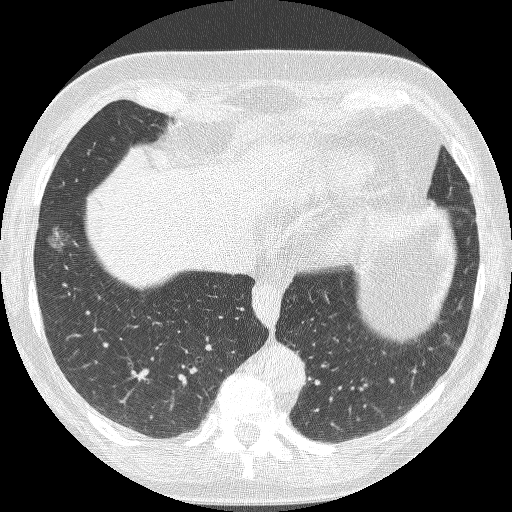
Axial slice from a low-dose chest CT screening exam; baseline screening round; lung window (W 1500 / L -600 HU); 1.25 mm slice thickness. Female participant, aged 68 years at enrolment. Current smoker at enrolment.
Expert reader's lesion annotation, bounding box <35,218,87,267> (left, top, right, bottom; pixels). Reader record for this screening exam (exam-level; its link to the box is not recorded): non-calcified nodule or mass ≥4 mm, right lower lobe, 16 × 12 mm, poorly defined margins, ground glass attenuation. Official screen result: positive, change unspecified: nodule(s) >= 4 mm or enlarging nodule(s), mass(es), or other non-specific abnormalities suspicious for lung cancer. Participant outcome: lung cancer diagnosed 406 days after this screen — bronchiolo-alveolar adenocarcinoma, NOS, right lower lobe, well differentiated (G1), stage IA (AJCC 6th edition), 13 mm at pathology.